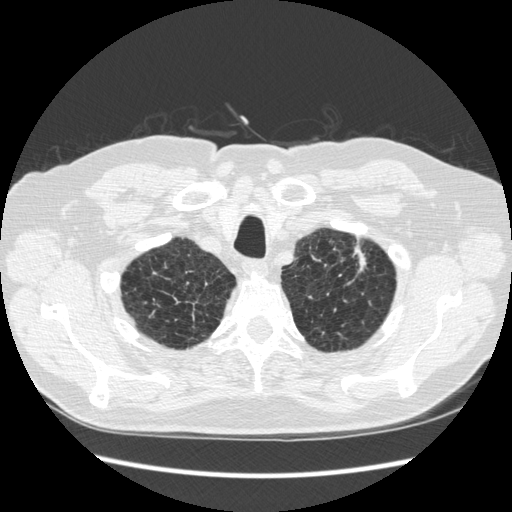
Axial slice from a low-dose chest CT screening exam, third annual screen, lung window (W 1500 / L -600 HU), 1.25 mm slice thickness, 120 kVp, slice 30 of 267 in the series, 512 × 512 image matrix. Male, age 70 years at enrolment.
• Expert-annotated lung lesion, bounding box [x1, y1, x2, y2] px = [324, 234, 380, 299].
• The screening reader recorded 2 non-calcified nodules or masses ≥4 mm on this exam (left upper lobe, right lower lobe); which of them this box marks is not recorded.
• Official screen result: positive, other.
• Participant outcome: lung cancer diagnosed 92 days after this screen — squamous cell carcinoma, NOS, left upper lobe, moderately differentiated (G2), stage IA (AJCC 6th edition), 18 mm at pathology.